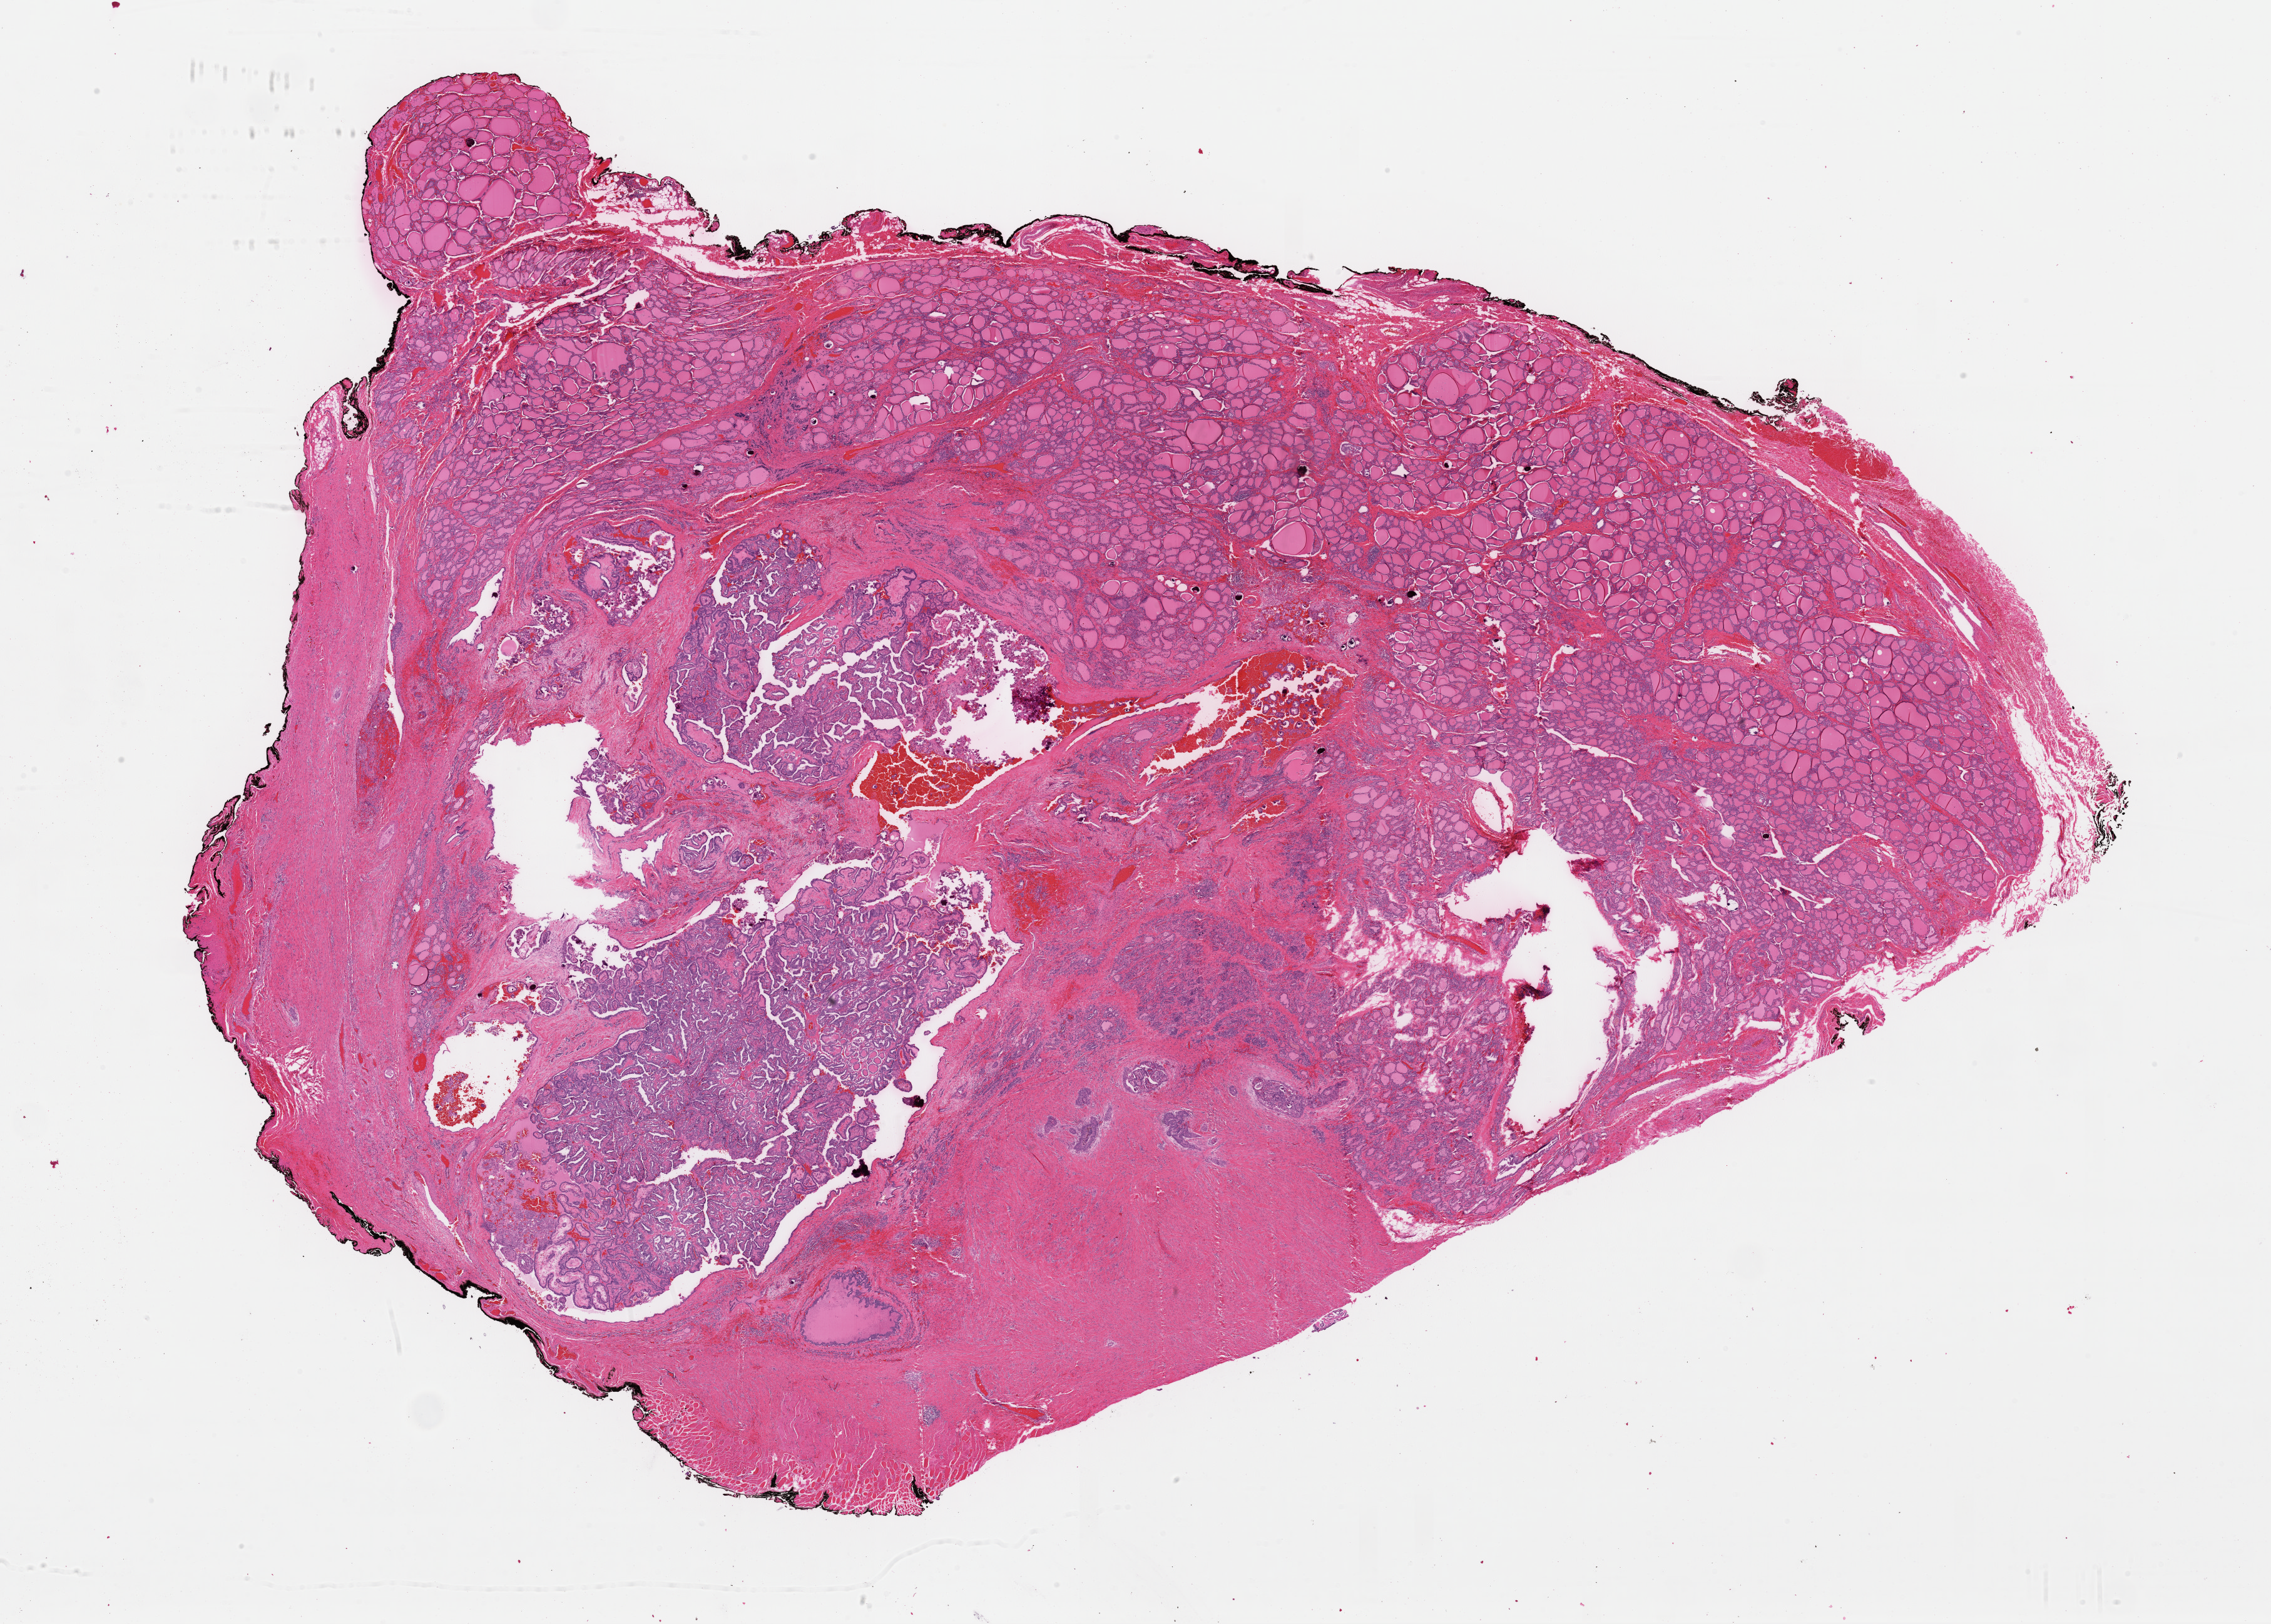
Whole-slide histology image, H&E-stained — low-resolution overview of the scanned area, about 28.7 x 20.5 mm. Formalin-fixed paraffin-embedded (FFPE) diagnostic section. Thyroid, primary tumour sample. Female, age 23 years at initial diagnosis.
* AJCC pathologic stage: I (6th edition)
* pathologic diagnosis: Papillary adenocarcinoma, NOS (thyroid gland)